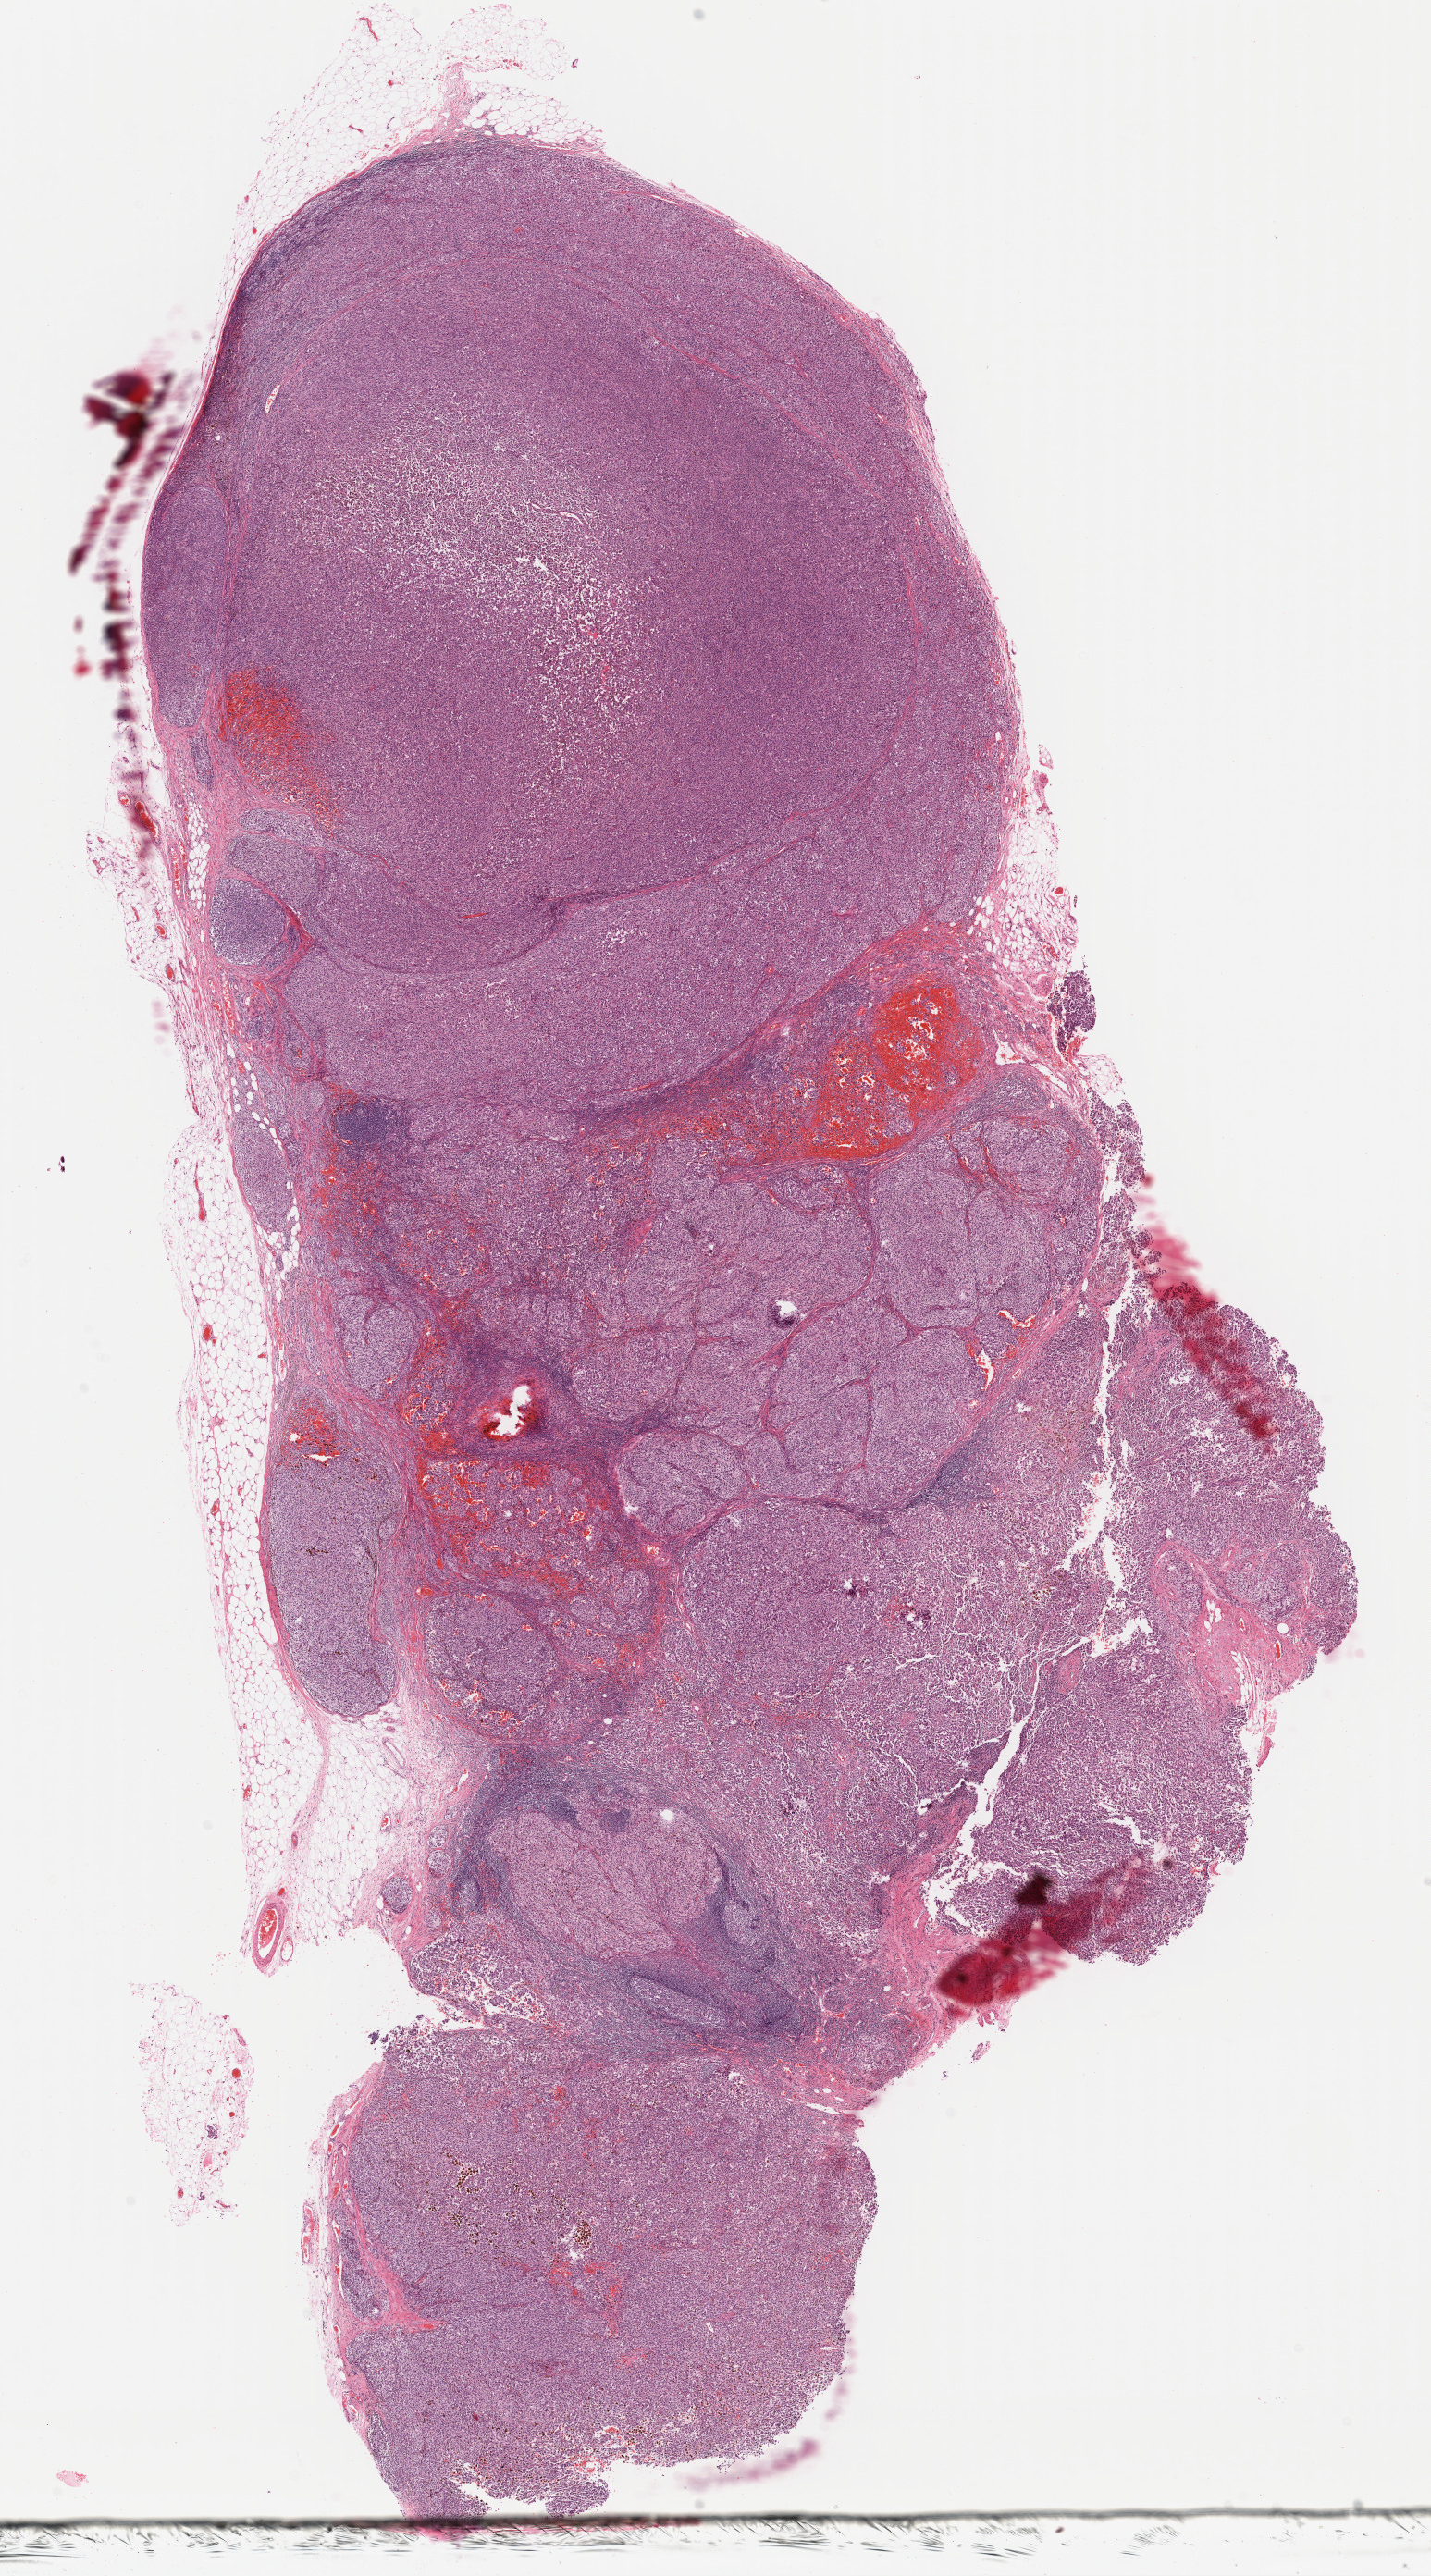
Digitized H&E tissue section (whole slide) — low-resolution overview of the scanned area, about 12.2 x 21.9 mm, FFPE section, metastatic tumour sample, sampled site: lymph node. Female, age 60 years at initial diagnosis.
* this section: metastatic tumour tissue
* patient diagnosis: Malignant melanoma, NOS